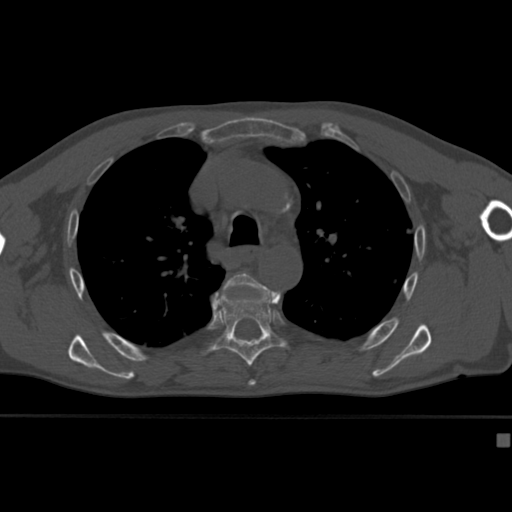
CT including the spine, one axial slice; position 297 of 430 along the scan axis; reconstruction kernel Br40s; bone window (W 1800 / L 400 HU); 1.5 mm slice thickness; 512 × 512 image matrix. Patient: male, 64 years. Case-level facts recorded for this patient, not image findings: primary cancer: uterus; vertebrae with lytic lesions (as recorded): T1, T4, T5, T7, L5.
Annotated regions visible in this slice (semi-automatically segmented with operator editing):
- T5 vertebra: bounding box <223,272,279,382> (left, top, right, bottom; pixels)
- T6 vertebra: <201,287,287,367>